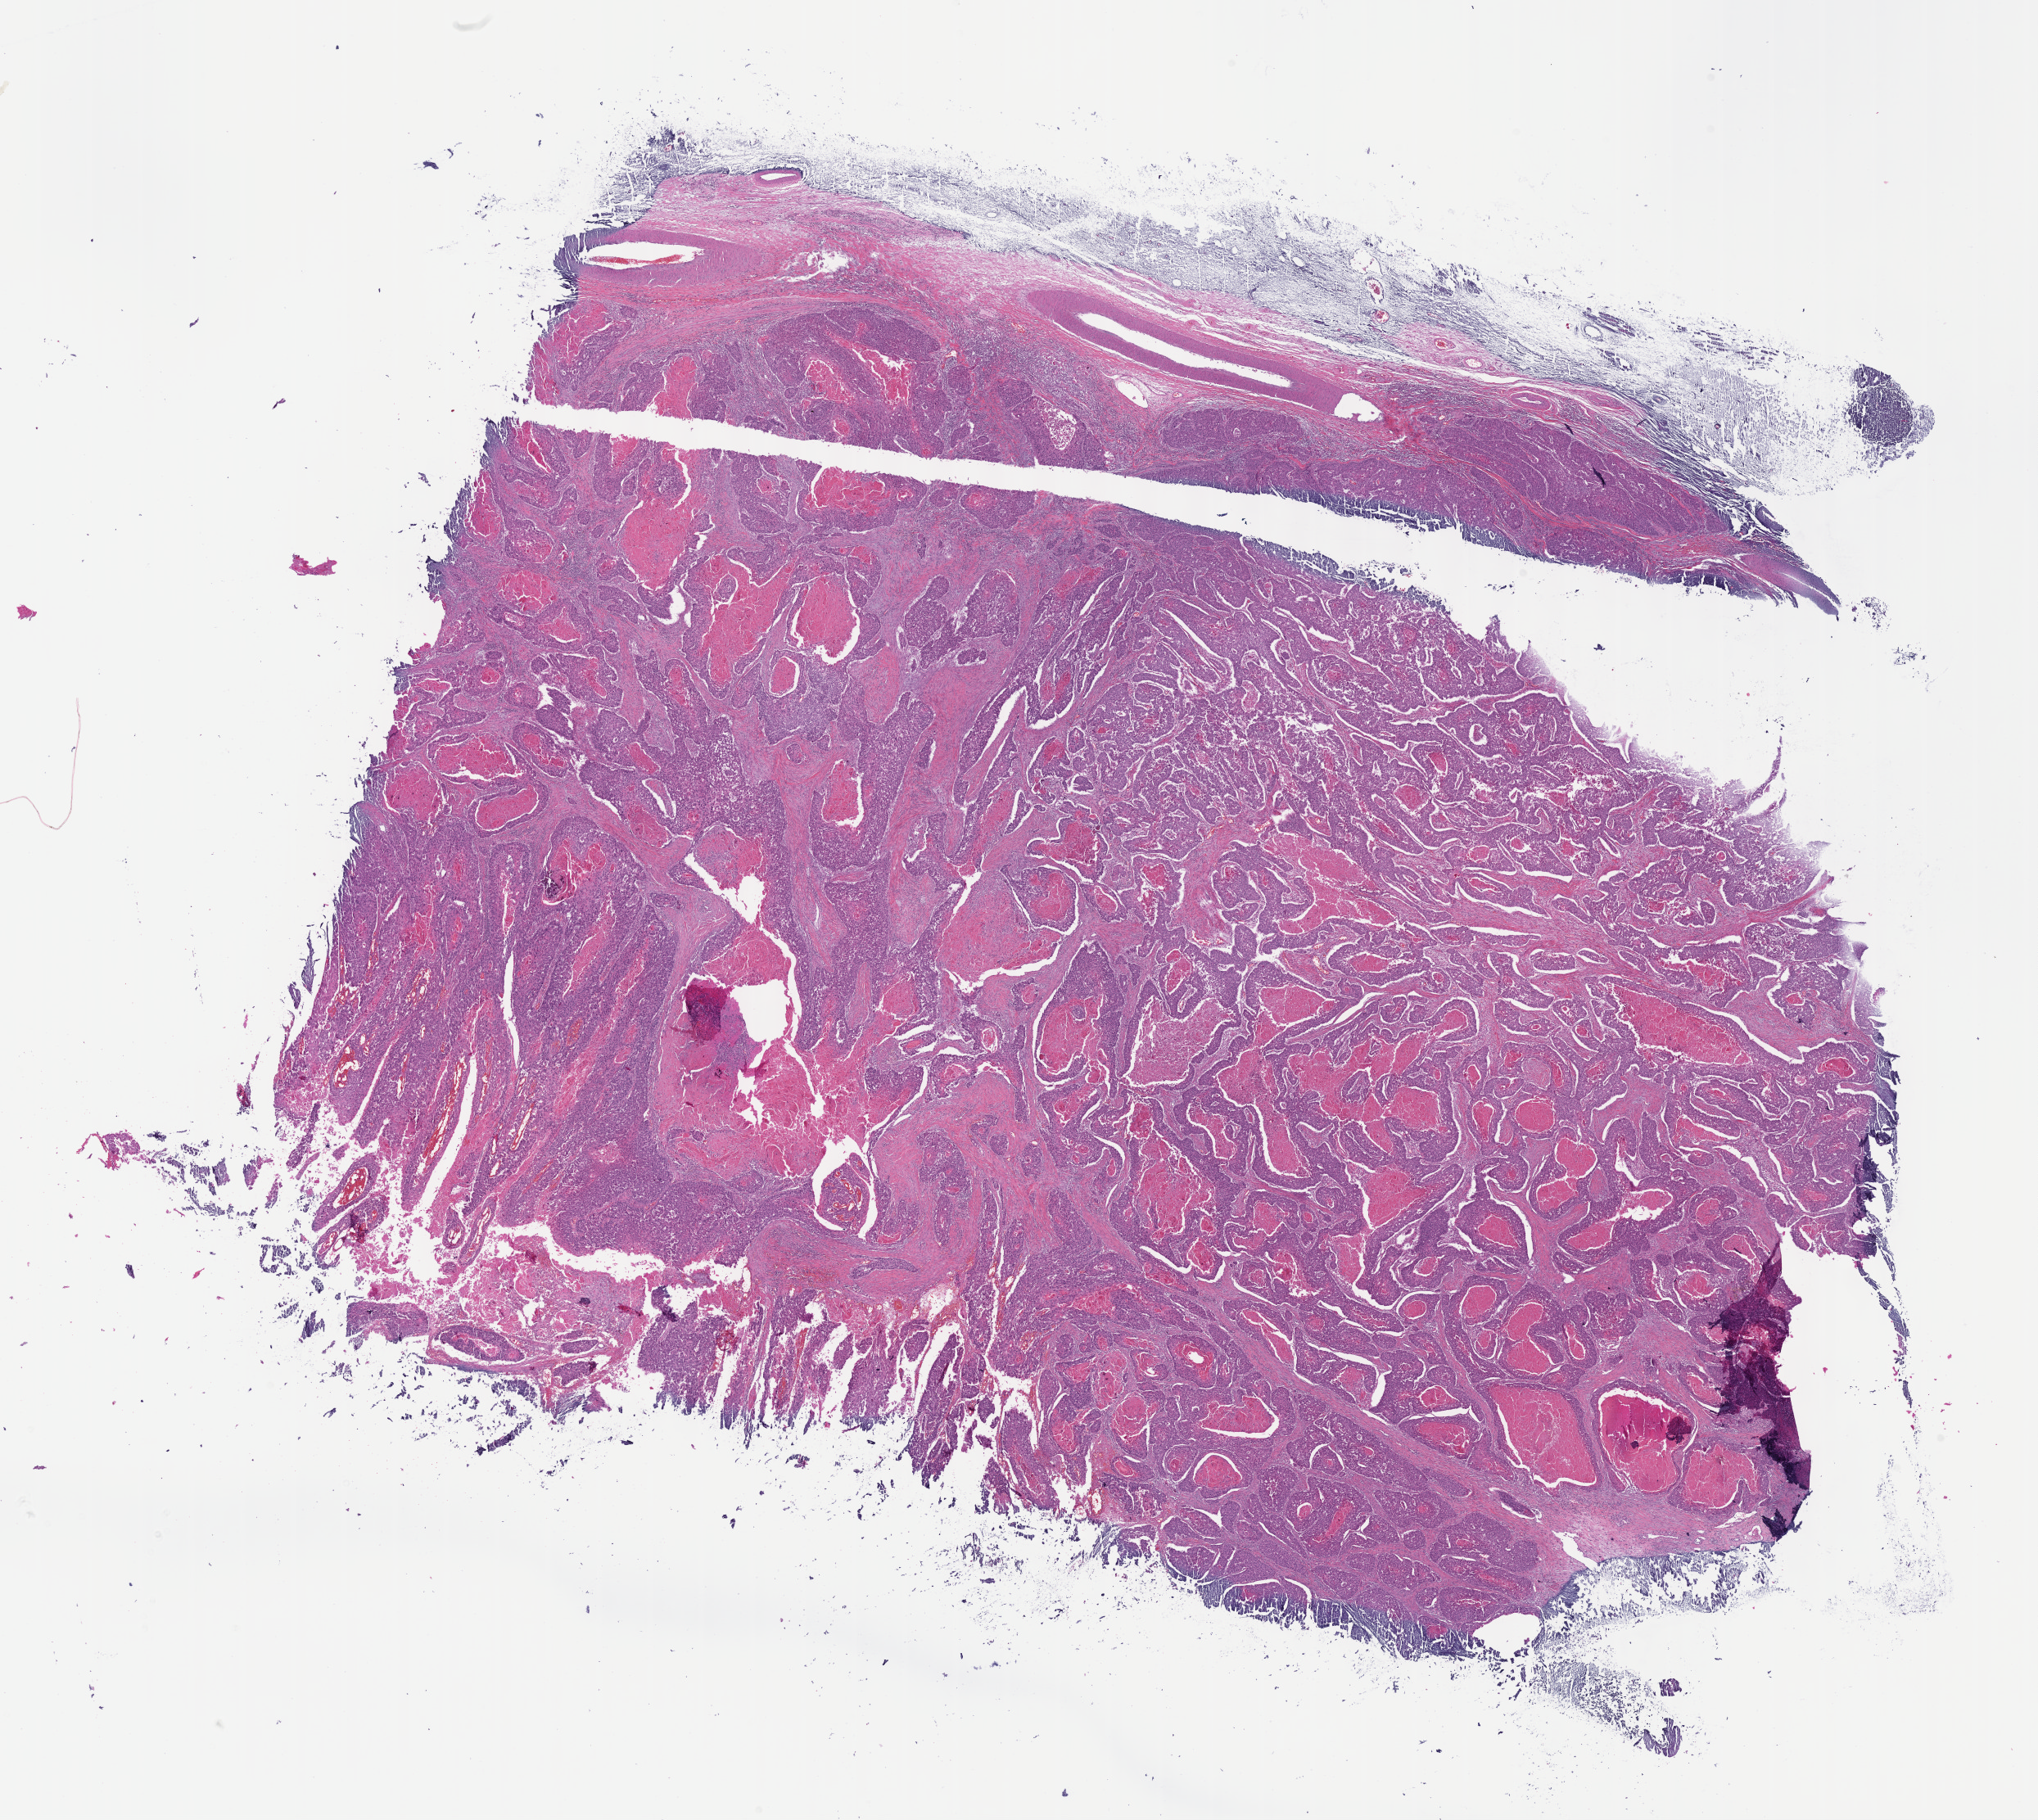
Hematoxylin and eosin (H&E) stained whole-slide image, low-resolution overview of the scanned area, about 20.1 x 18.0 mm, formalin-fixed paraffin-embedded (FFPE) diagnostic section, head and neck, primary tumour sample. Male patient; age at initial diagnosis 62 years. Histologic grade: G2 (moderately differentiated).
Diagnosis: Squamous cell carcinoma, NOS. Lymph nodes positive (case pathology): 2 of 28 examined. AJCC pathologic stage: IVA (7th edition).